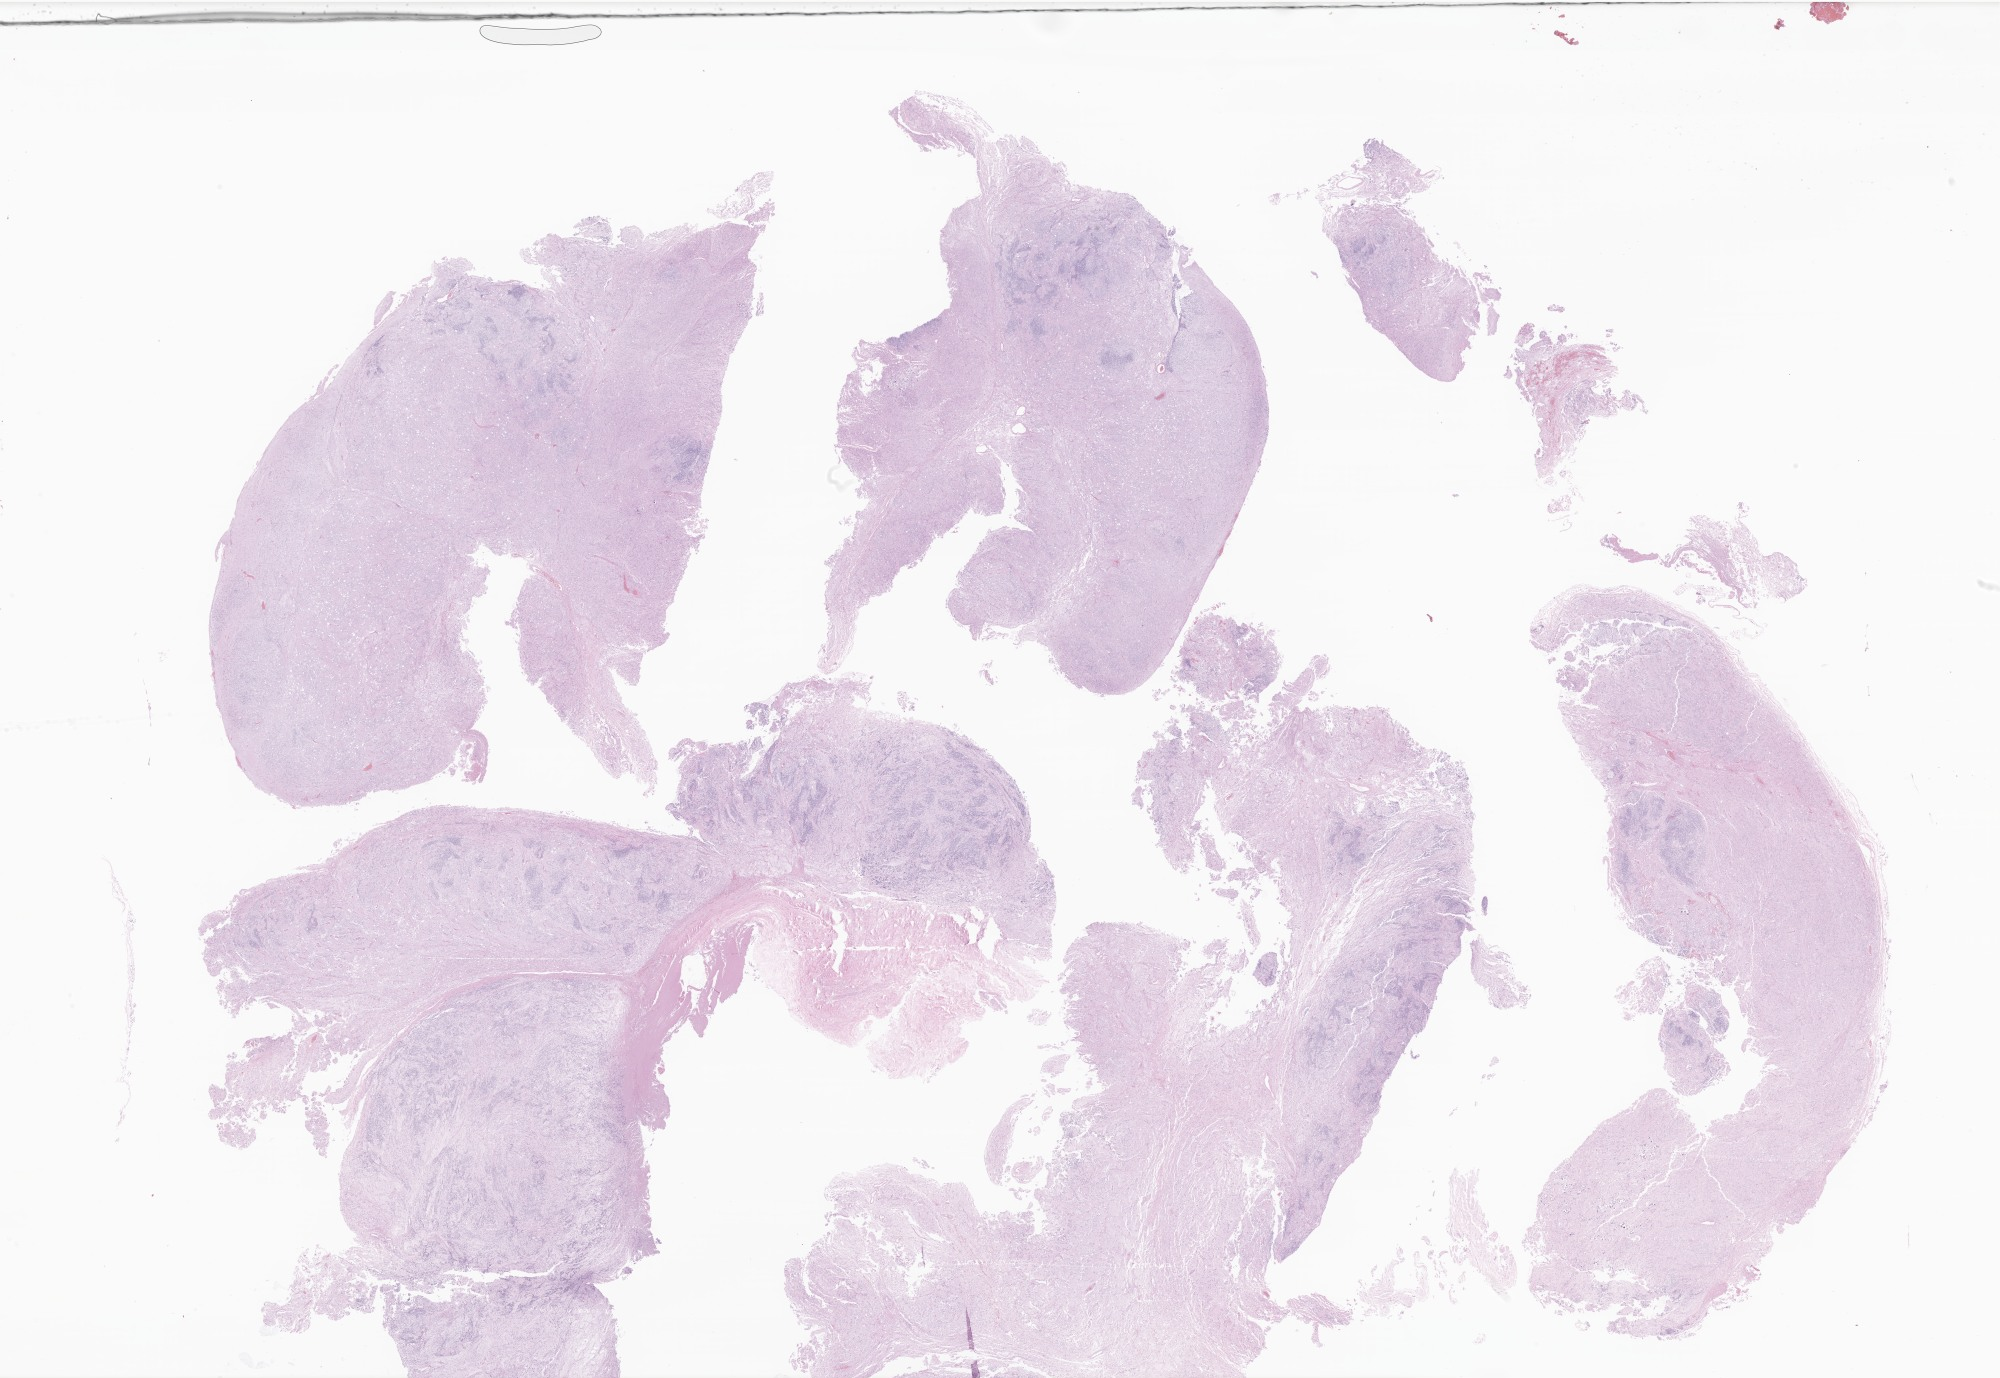
Hematoxylin and eosin (H&E) whole-slide image of tumor tissue from the brain — whole scanned area (about 33.7 x 23.2 mm) shown as a low-resolution overview, formalin-fixed, paraffin-embedded (FFPE) tissue. Patient: female, age 92 months.
Recorded diagnosis: Neoplasm, malignant.